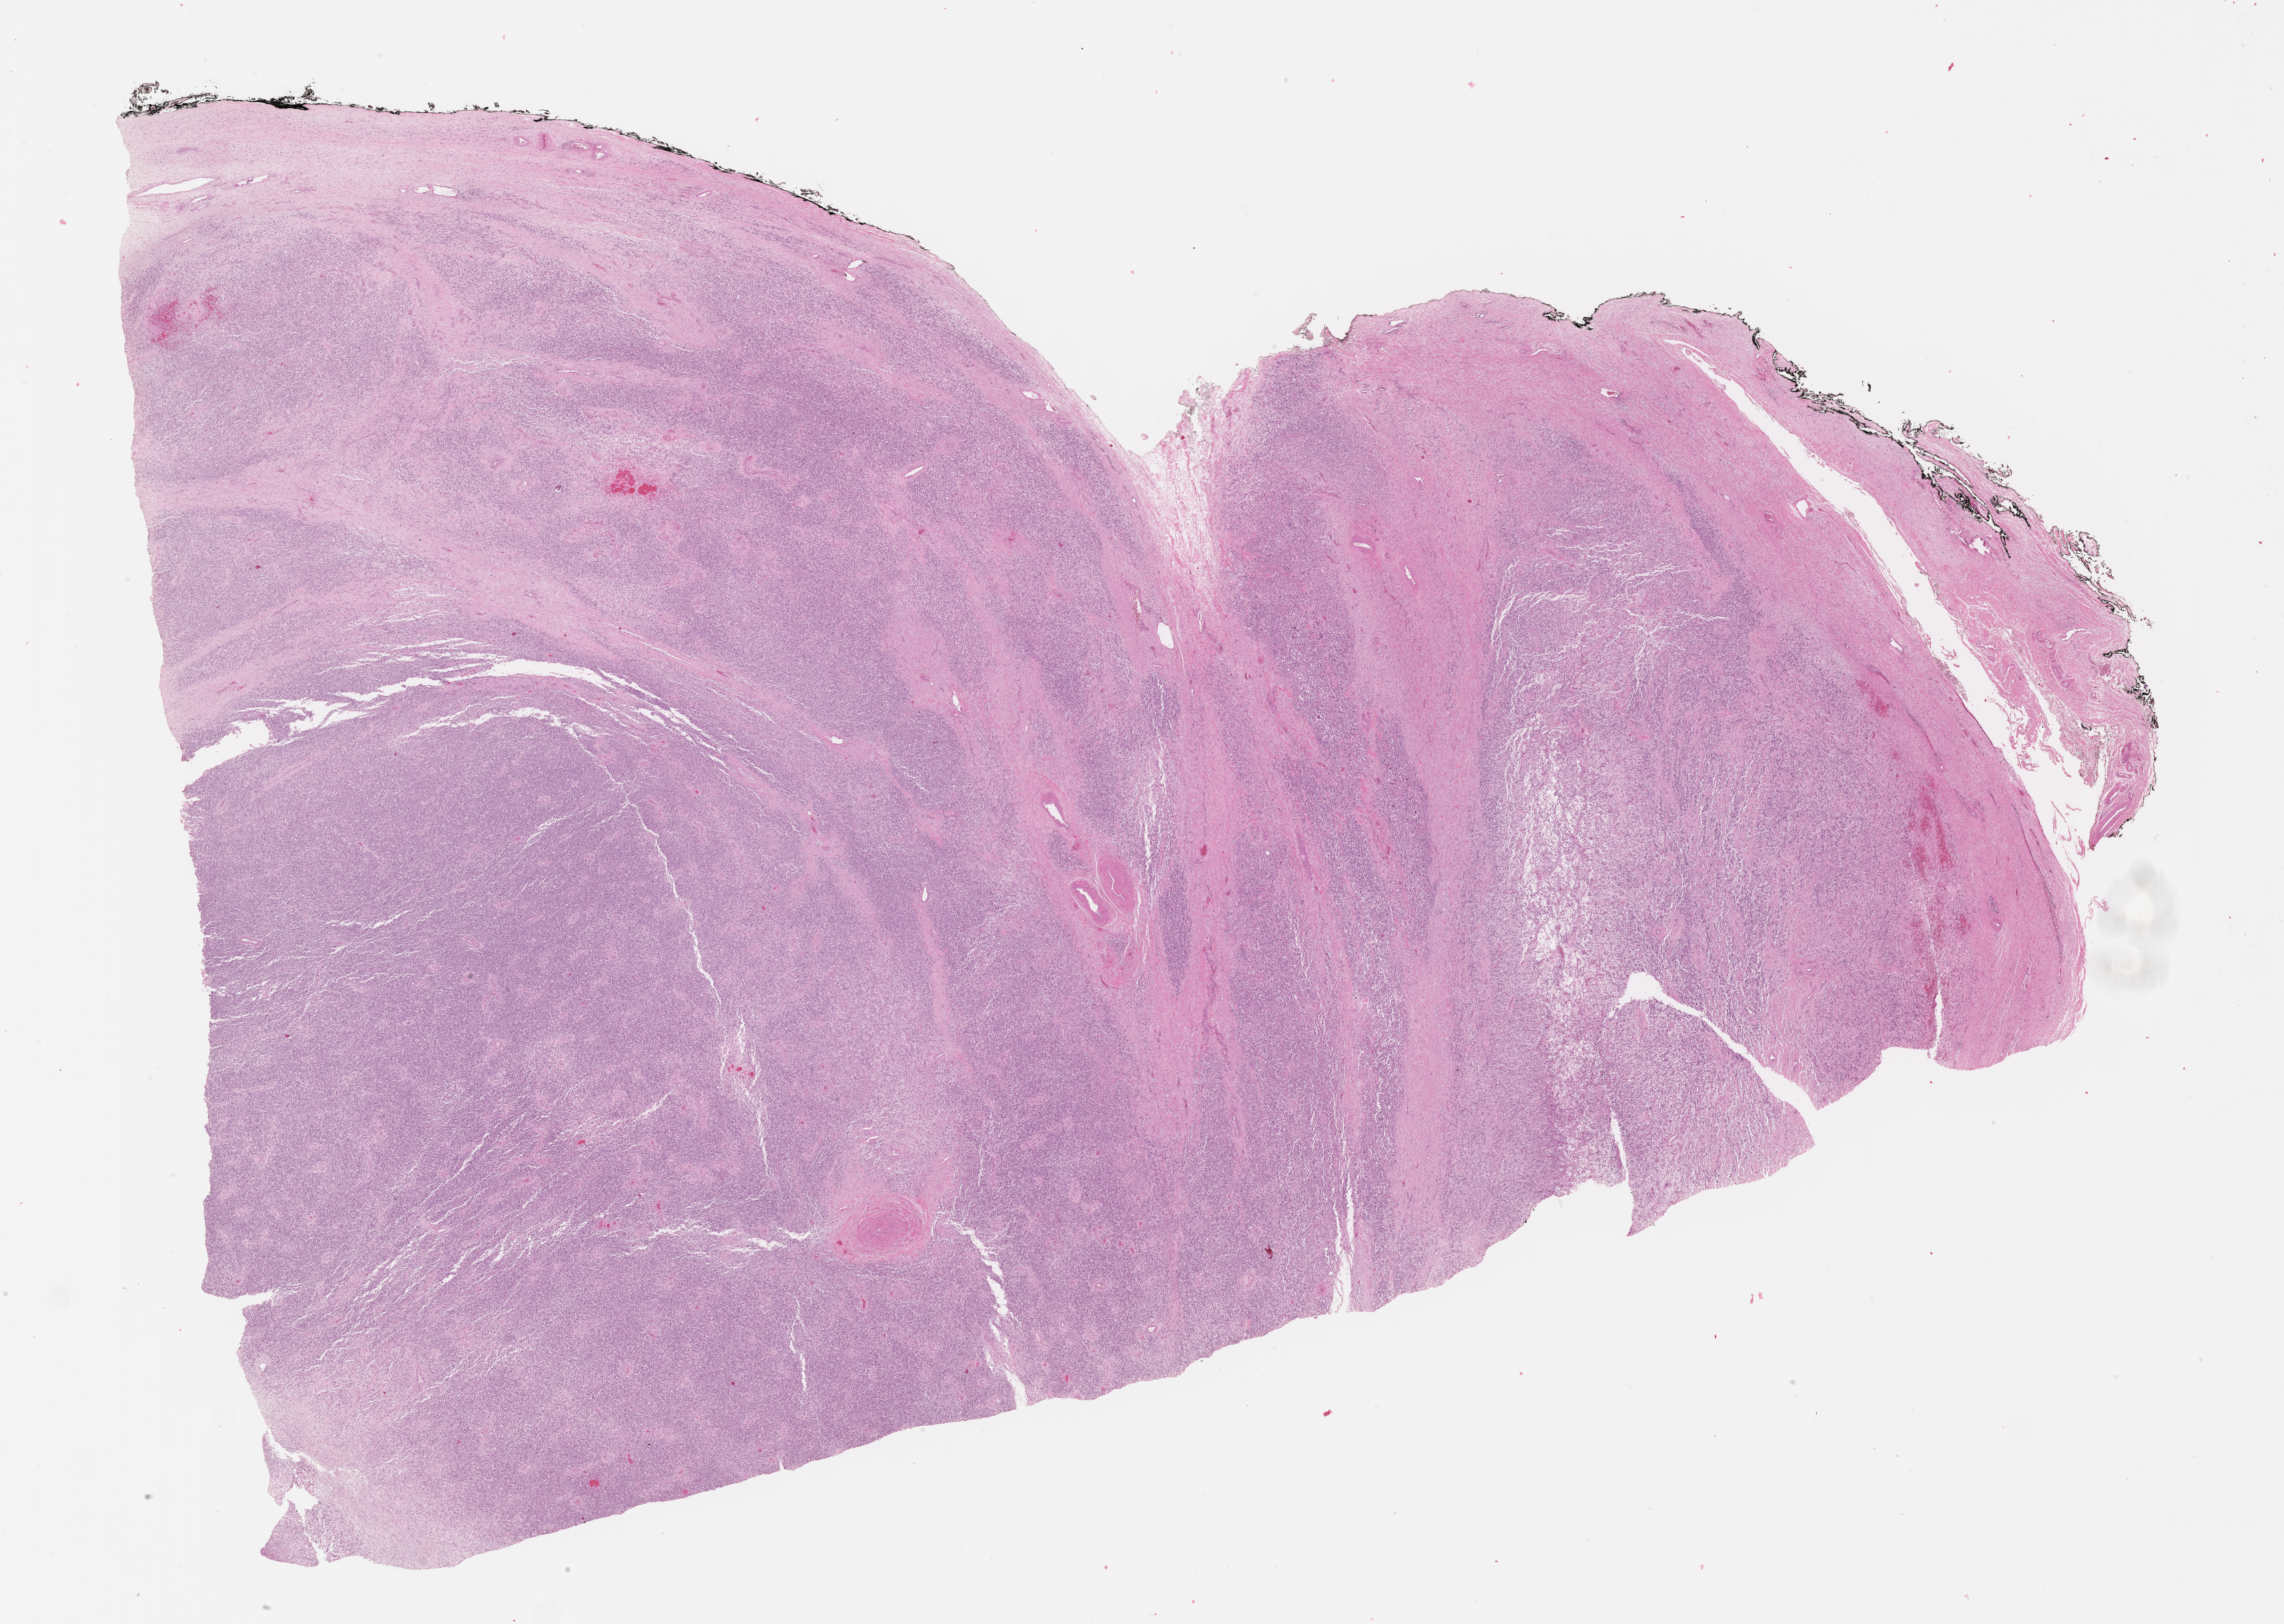
Digitized haematoxylin and eosin-stained section of tumor tissue — a low-resolution overview of the entire scanned area, about 27.7 x 19.7 mm, formalin-fixed, paraffin-embedded (FFPE) tissue, sample anatomic site: testicle, right. Male patient, age at diagnosis 17.1 years.
• stage (as recorded): 1
• metastatic status at presentation (as recorded): non-metastatic (confirmed)
• primary site (case record): testis-paratesticular
• diagnosis: rhabdomyosarcoma; histological classification: embryonal rhabdomyosarcoma